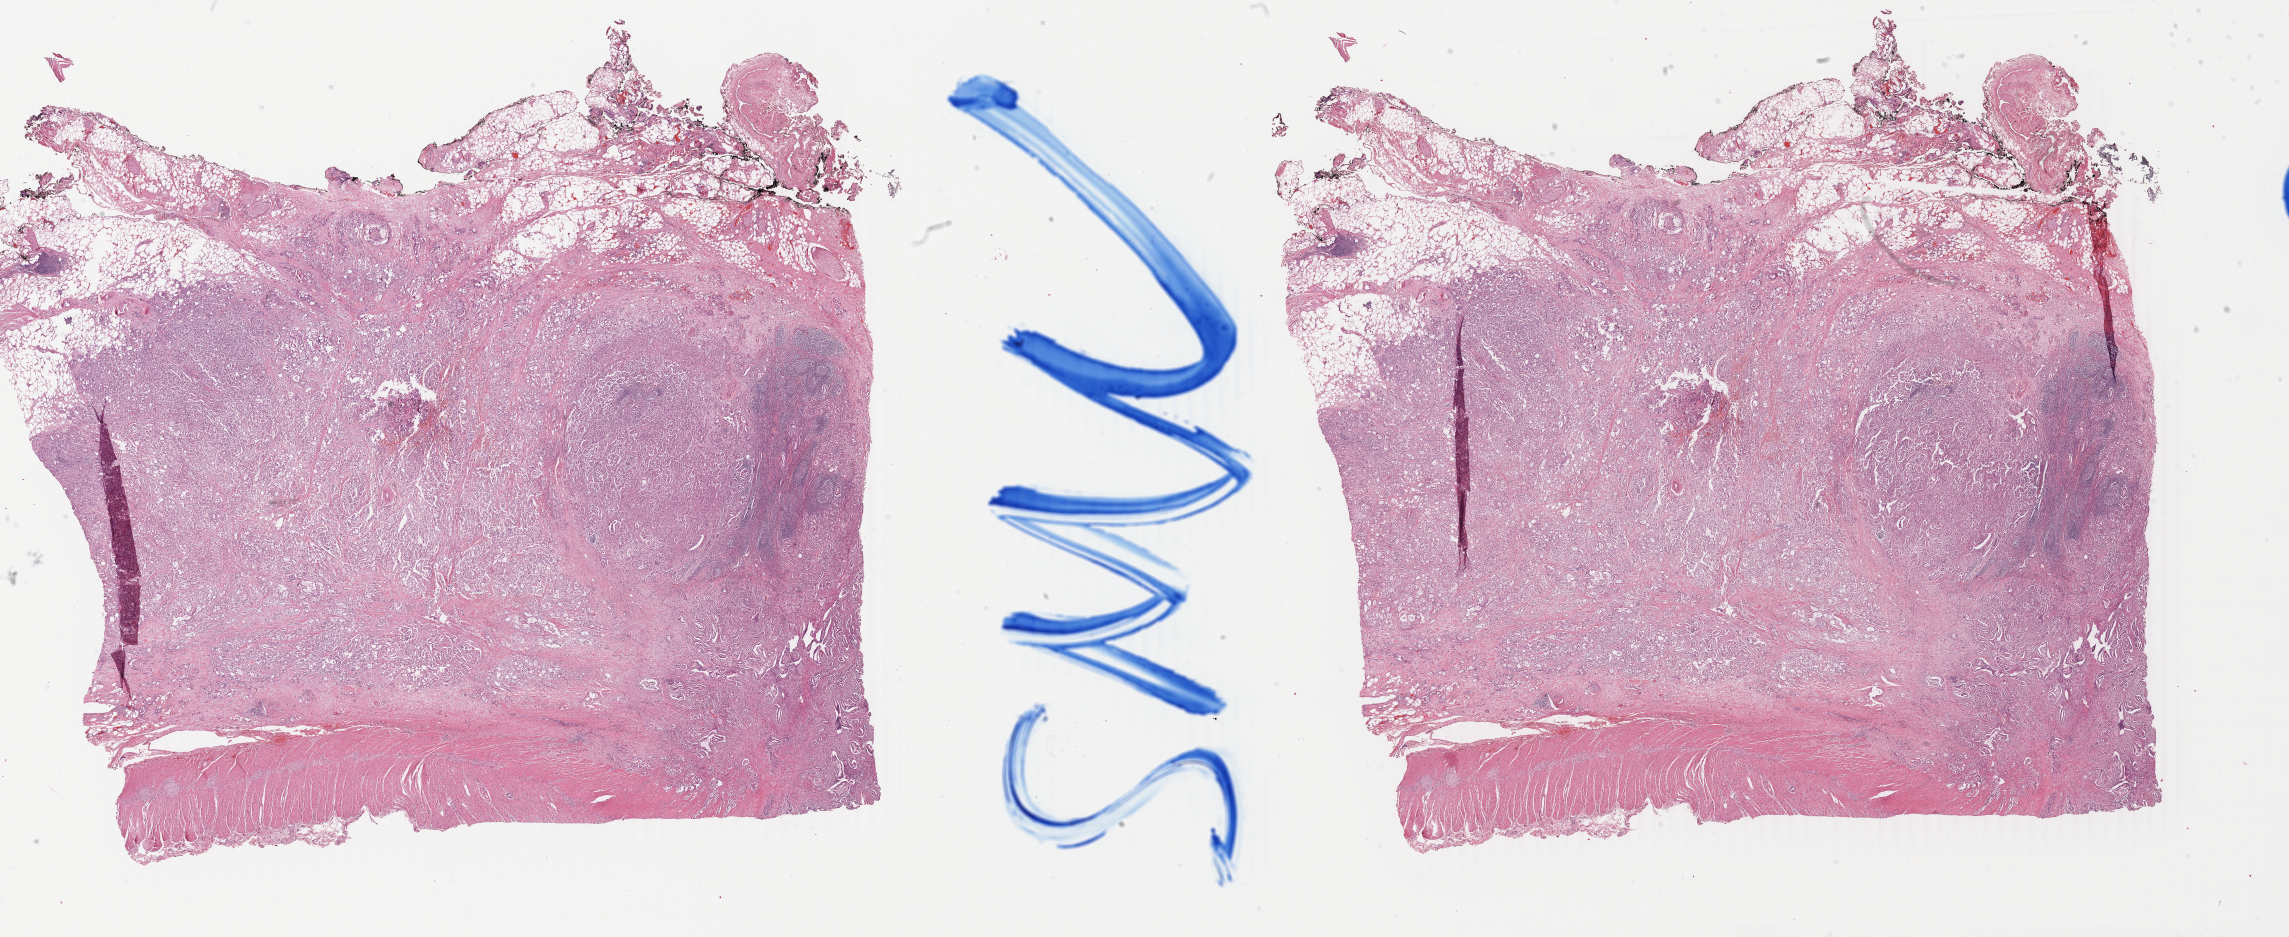
Digitized H&E tissue section (whole slide) — a low-resolution overview of the entire scanned area, about 36.4 x 14.9 mm (slide scanned at 40x). Formalin-fixed paraffin-embedded (FFPE) diagnostic section. Pancreas, primary tumour sample. Patient: female, age at initial diagnosis 44 years. Histologic grade: G3 (poorly differentiated).
AJCC pathologic stage: IIB (7th edition). Lymph nodes positive (case pathology): 3 of 22 examined. Pathologic diagnosis: Infiltrating duct carcinoma, NOS (head of pancreas).